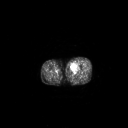
FDG PET of an extremity soft-tissue mass (from a PET/CT study), one axial slice; 3.27 mm slice thickness; 128 × 128 image matrix, field of view 700 × 700 mm. Male patient, age 48 years. Case-level facts recorded for this patient, not image findings: histological type: pleiomorphic leiomyosarcoma; grade: high; site of the primary tumour: left thigh.
Annotated regions visible in this slice (expert contour drawn on MRI and transferred to this co-registered scan by the dataset authors):
- gross tumour volume including surrounding oedema: bounding box <69,63,77,71> (left, top, right, bottom; pixels)
- gross tumour volume (mass): <70,64,75,71>